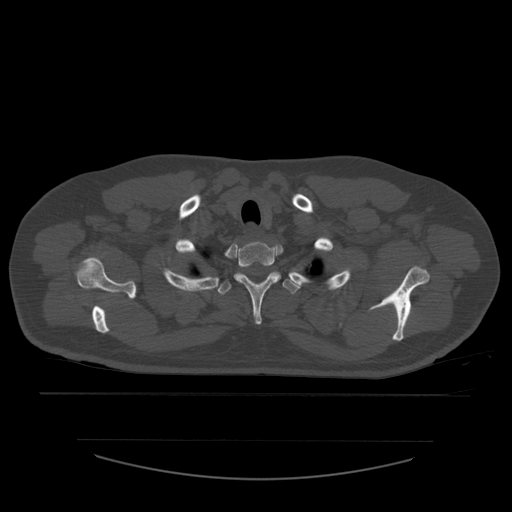
CT including the spine, one axial slice. Slice 463 of 532 in the series (ordered by position). 120 kVp. Bone window (W 1800 / L 400 HU). 1.25 mm slice thickness. 512 × 512 image matrix, field of view 441 × 441 mm. Patient age 44 years. From the clinical record (not read from this slice): primary cancer: soft tissue sarcoma.
Outlined on this slice (semi-automatically segmented with operator editing):
- T1 vertebra: box from (x=234, y=242) to (x=281, y=325) px
- T2 vertebra: (x=218, y=271)–(x=303, y=295)